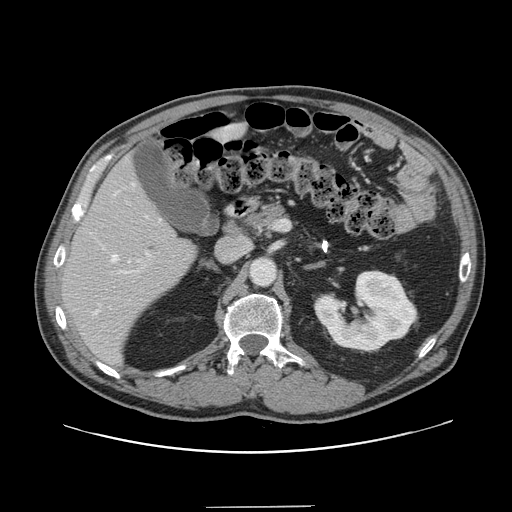
Contrast-enhanced abdominal CT, one axial slice. Position 79 of 139 along the scan axis. 120 kVp. Intravenous contrast given. Soft-tissue window (W 400 / L 40 HU). 2.5 mm slice thickness. 512 × 512 image matrix. Male patient, age 64 years. From the clinical record (not read from this slice): diagnosis: colorectal cancer liver metastases, imaged before liver resection.
Structures marked on this image (outlined manually by an expert reader):
- hepatic veins: bounding box [x1, y1, x2, y2] px = [93, 183, 161, 315]
- liver: [63, 126, 240, 364]
- planned liver remnant (the part of the liver to remain after resection): [63, 126, 240, 364]
- portal vein (with intrahepatic branches): [111, 252, 149, 274]